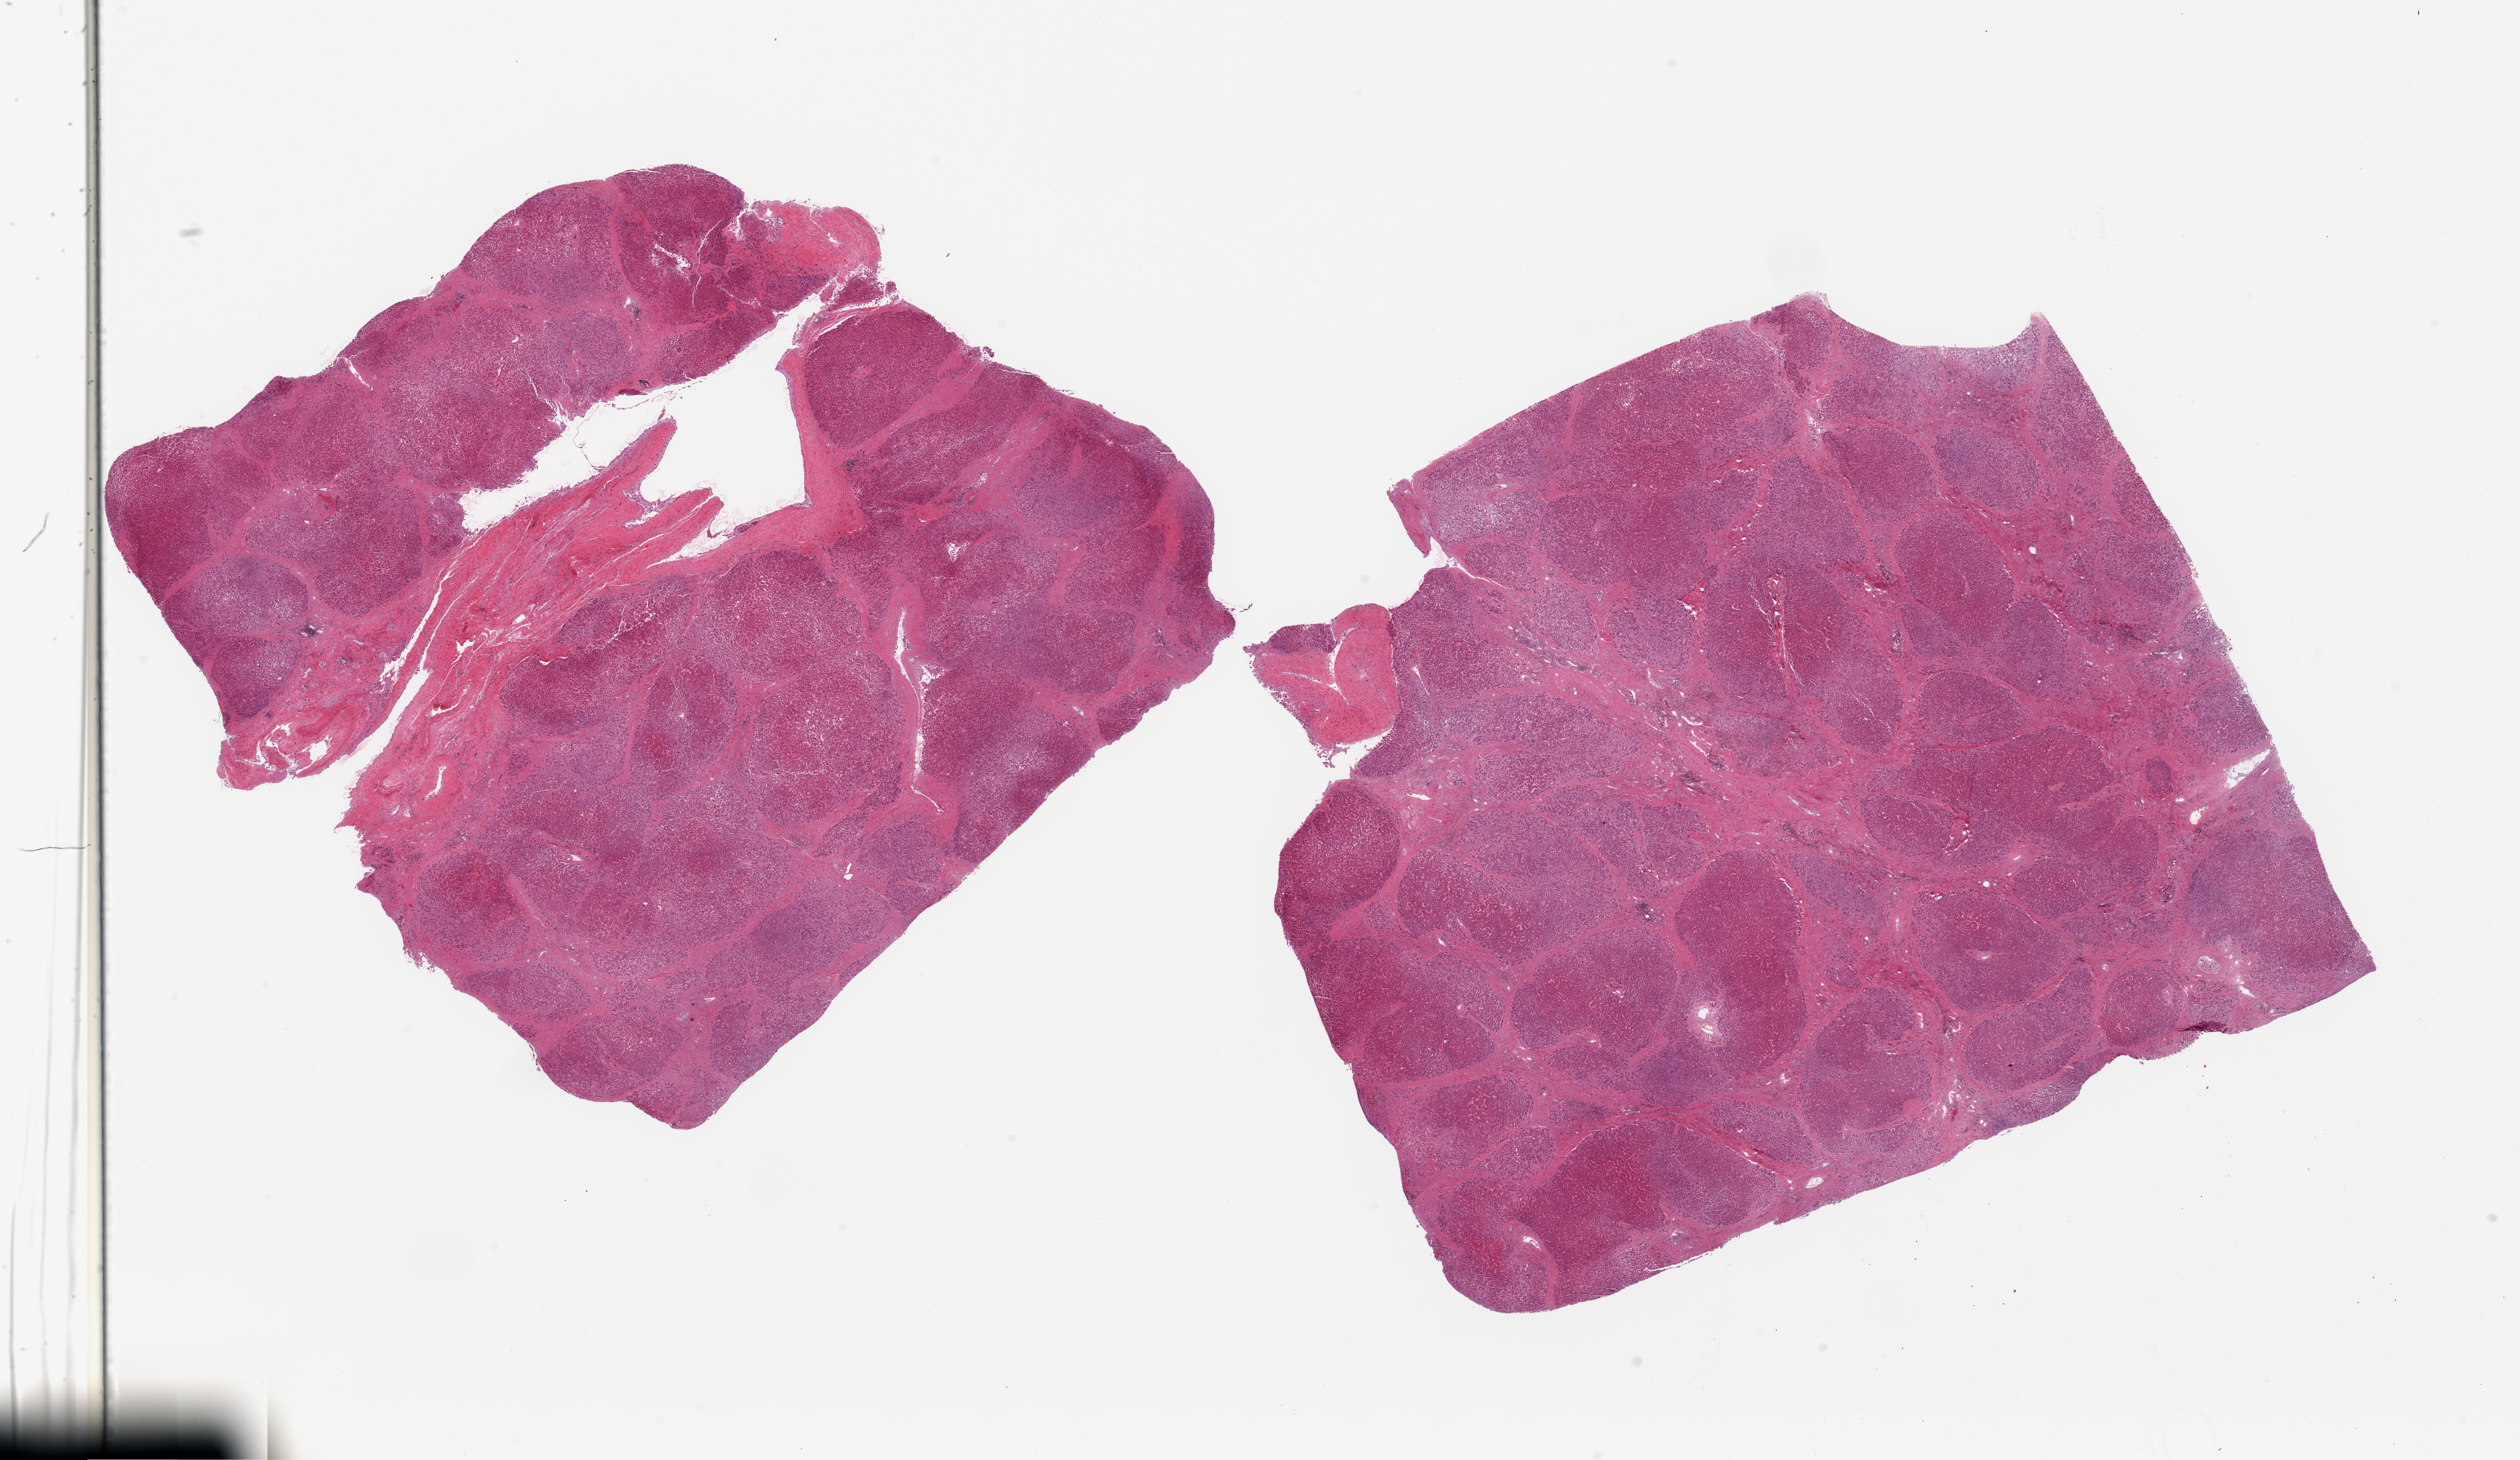
Hematoxylin and eosin (H&E) whole-slide image, shown as a low-resolution overview of the whole scanned area (about 27.6 x 16.0 mm, from a 20x scan), PAXgene-fixed paraffin-embedded (PFPE) section, section of liver (target tissue), tissue donor sample. Donor sex: male.
Reviewer comment on this tissue sample: 2 pieces, established cirrhosis.